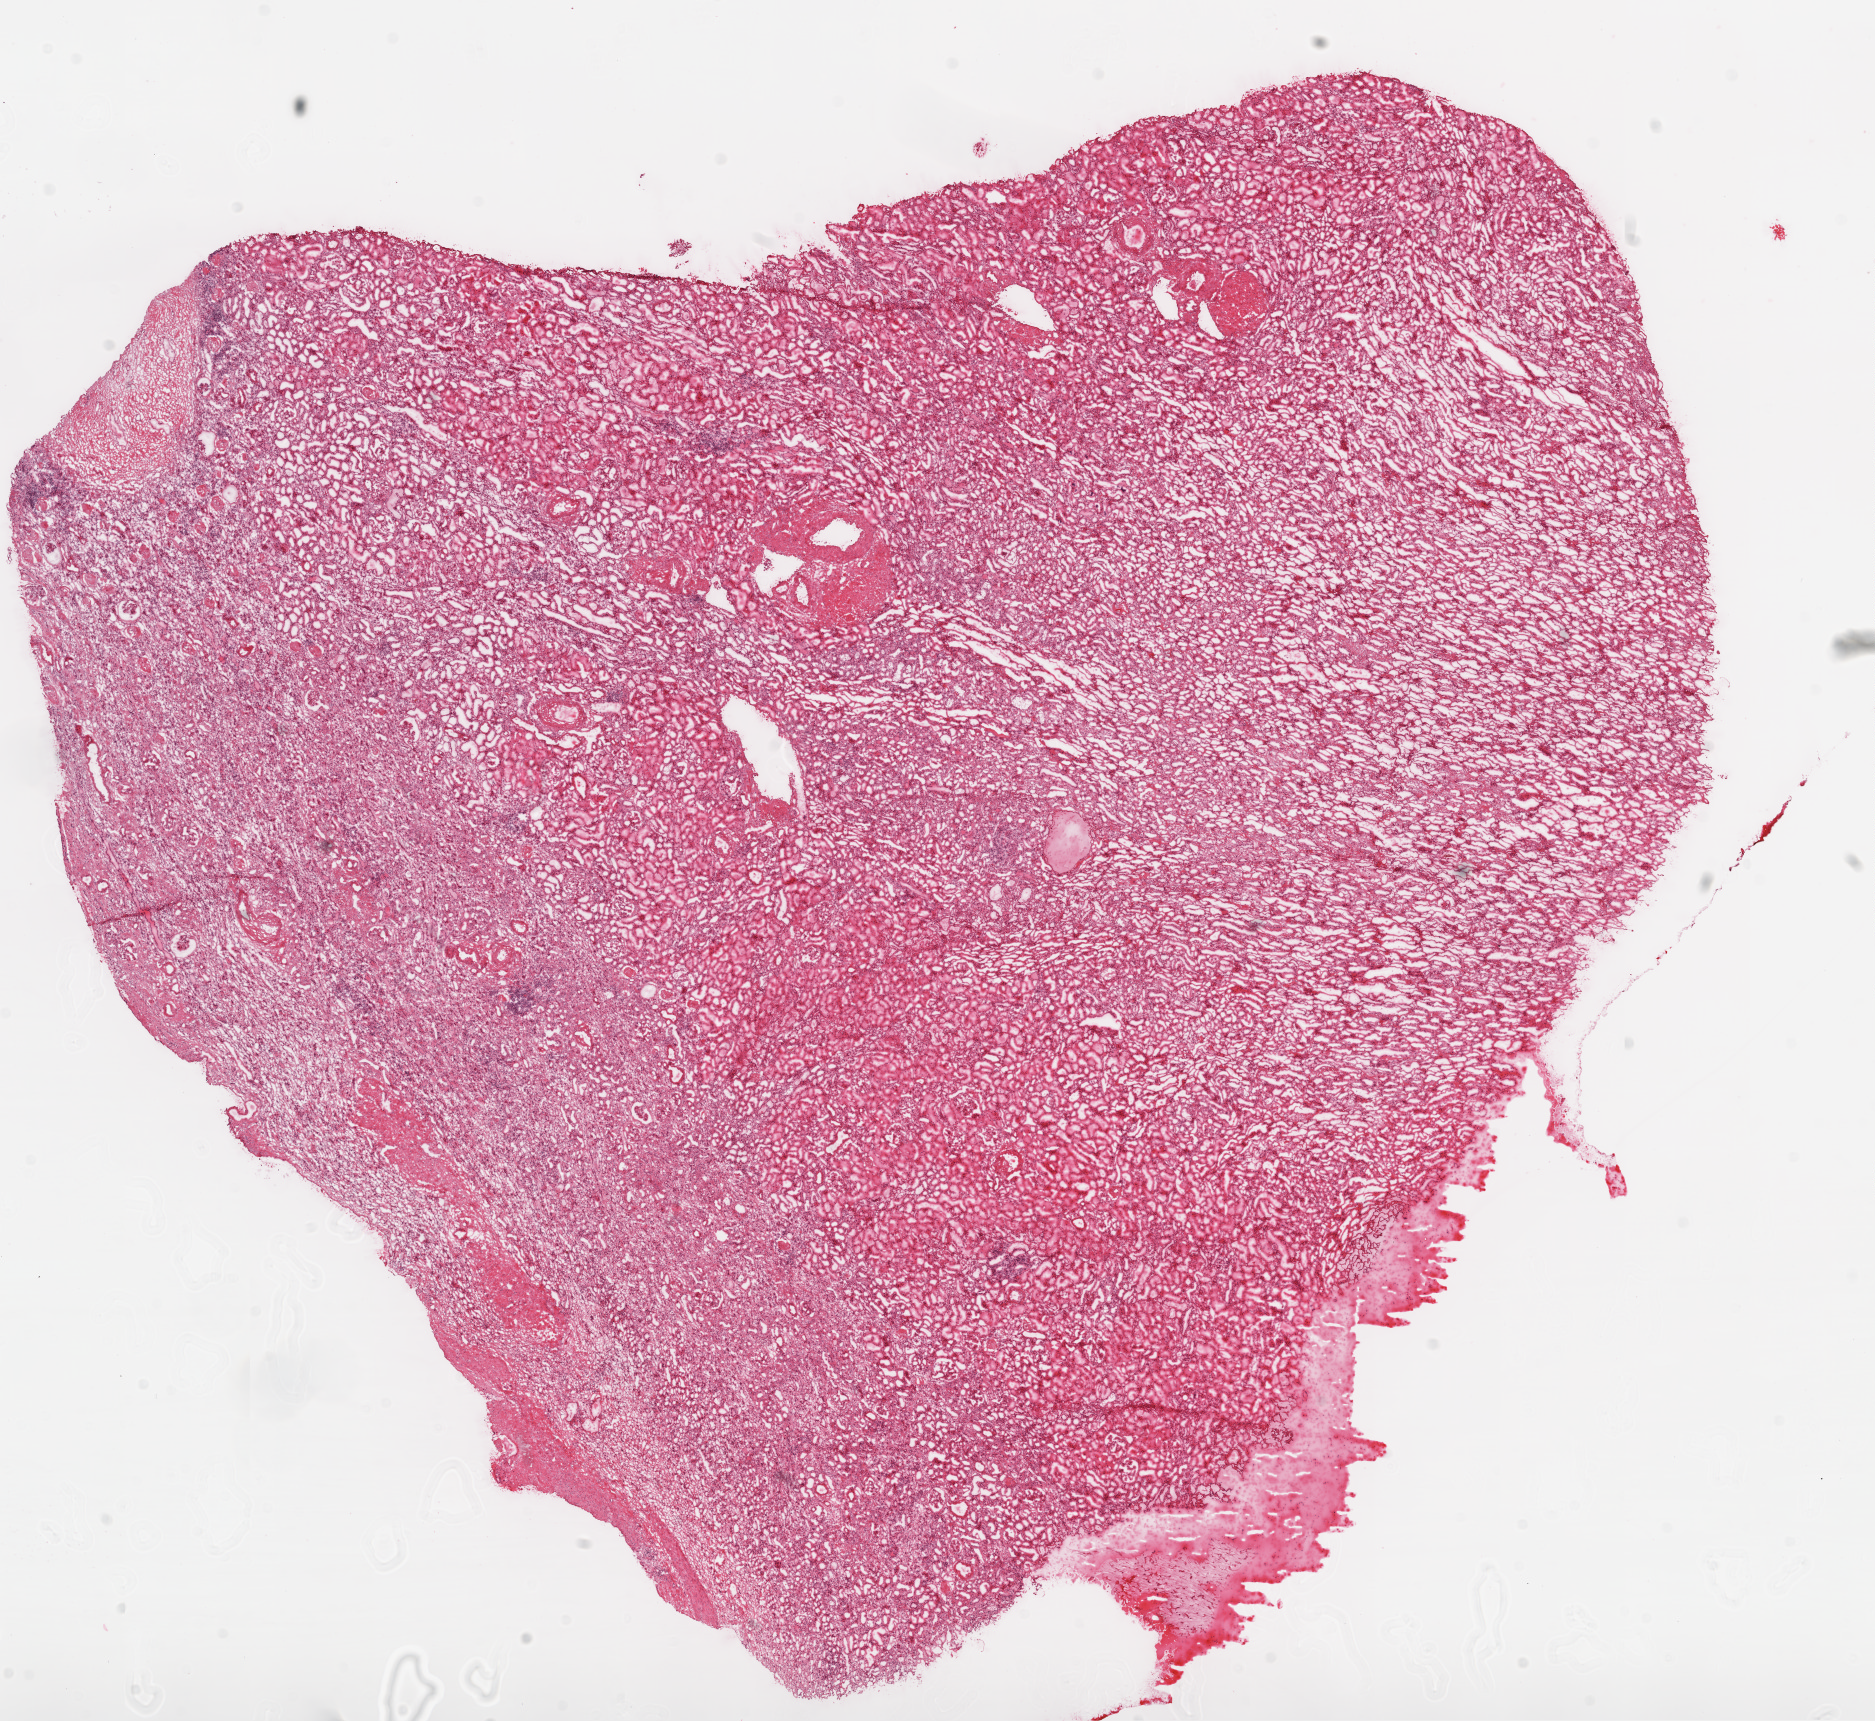
Digitized Hematoxylin and eosin (H&E) stained tissue section (whole slide) — whole scanned area (about 15.0 x 13.8 mm) shown as a low-resolution overview. Frozen section from the top of the tissue portion. Solid tissue normal (non-tumour tissue) sample from the kidney. Female patient; age at initial diagnosis 60 years.
This section: solid tissue normal sample (biorepository sample class). Patient diagnosis: Clear cell adenocarcinoma, NOS.